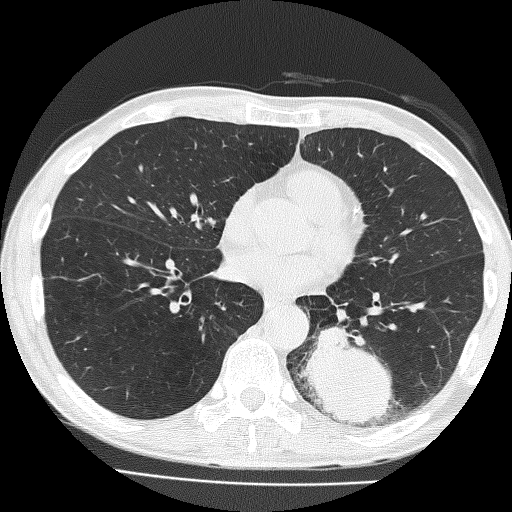
Axial slice from a low-dose chest CT screening exam, first (baseline) screen, lung window (W 1500 / L -600 HU), 2 mm slice thickness, lung (sharp) reconstruction kernel (FC51), slice 88 of 160 in the series, 512 × 512 image matrix. Male participant, aged 58 years at enrolment. Current smoker at enrolment.
Expert reader's lesion annotation, bounding box [x1, y1, x2, y2] px = [301, 311, 420, 434]. The screening reader recorded 2 non-calcified nodules or masses ≥4 mm on this exam (left lower lobe, left upper lobe); which of them this box marks is not recorded. Official screen result: positive, change unspecified: nodule(s) >= 4 mm or enlarging nodule(s), mass(es), or other non-specific abnormalities suspicious for lung cancer. Participant outcome: lung cancer diagnosed 39 days after this screen — non-small cell carcinoma, left lower lobe, poorly differentiated (G3), stage IV (AJCC 6th edition), 74 mm at pathology.